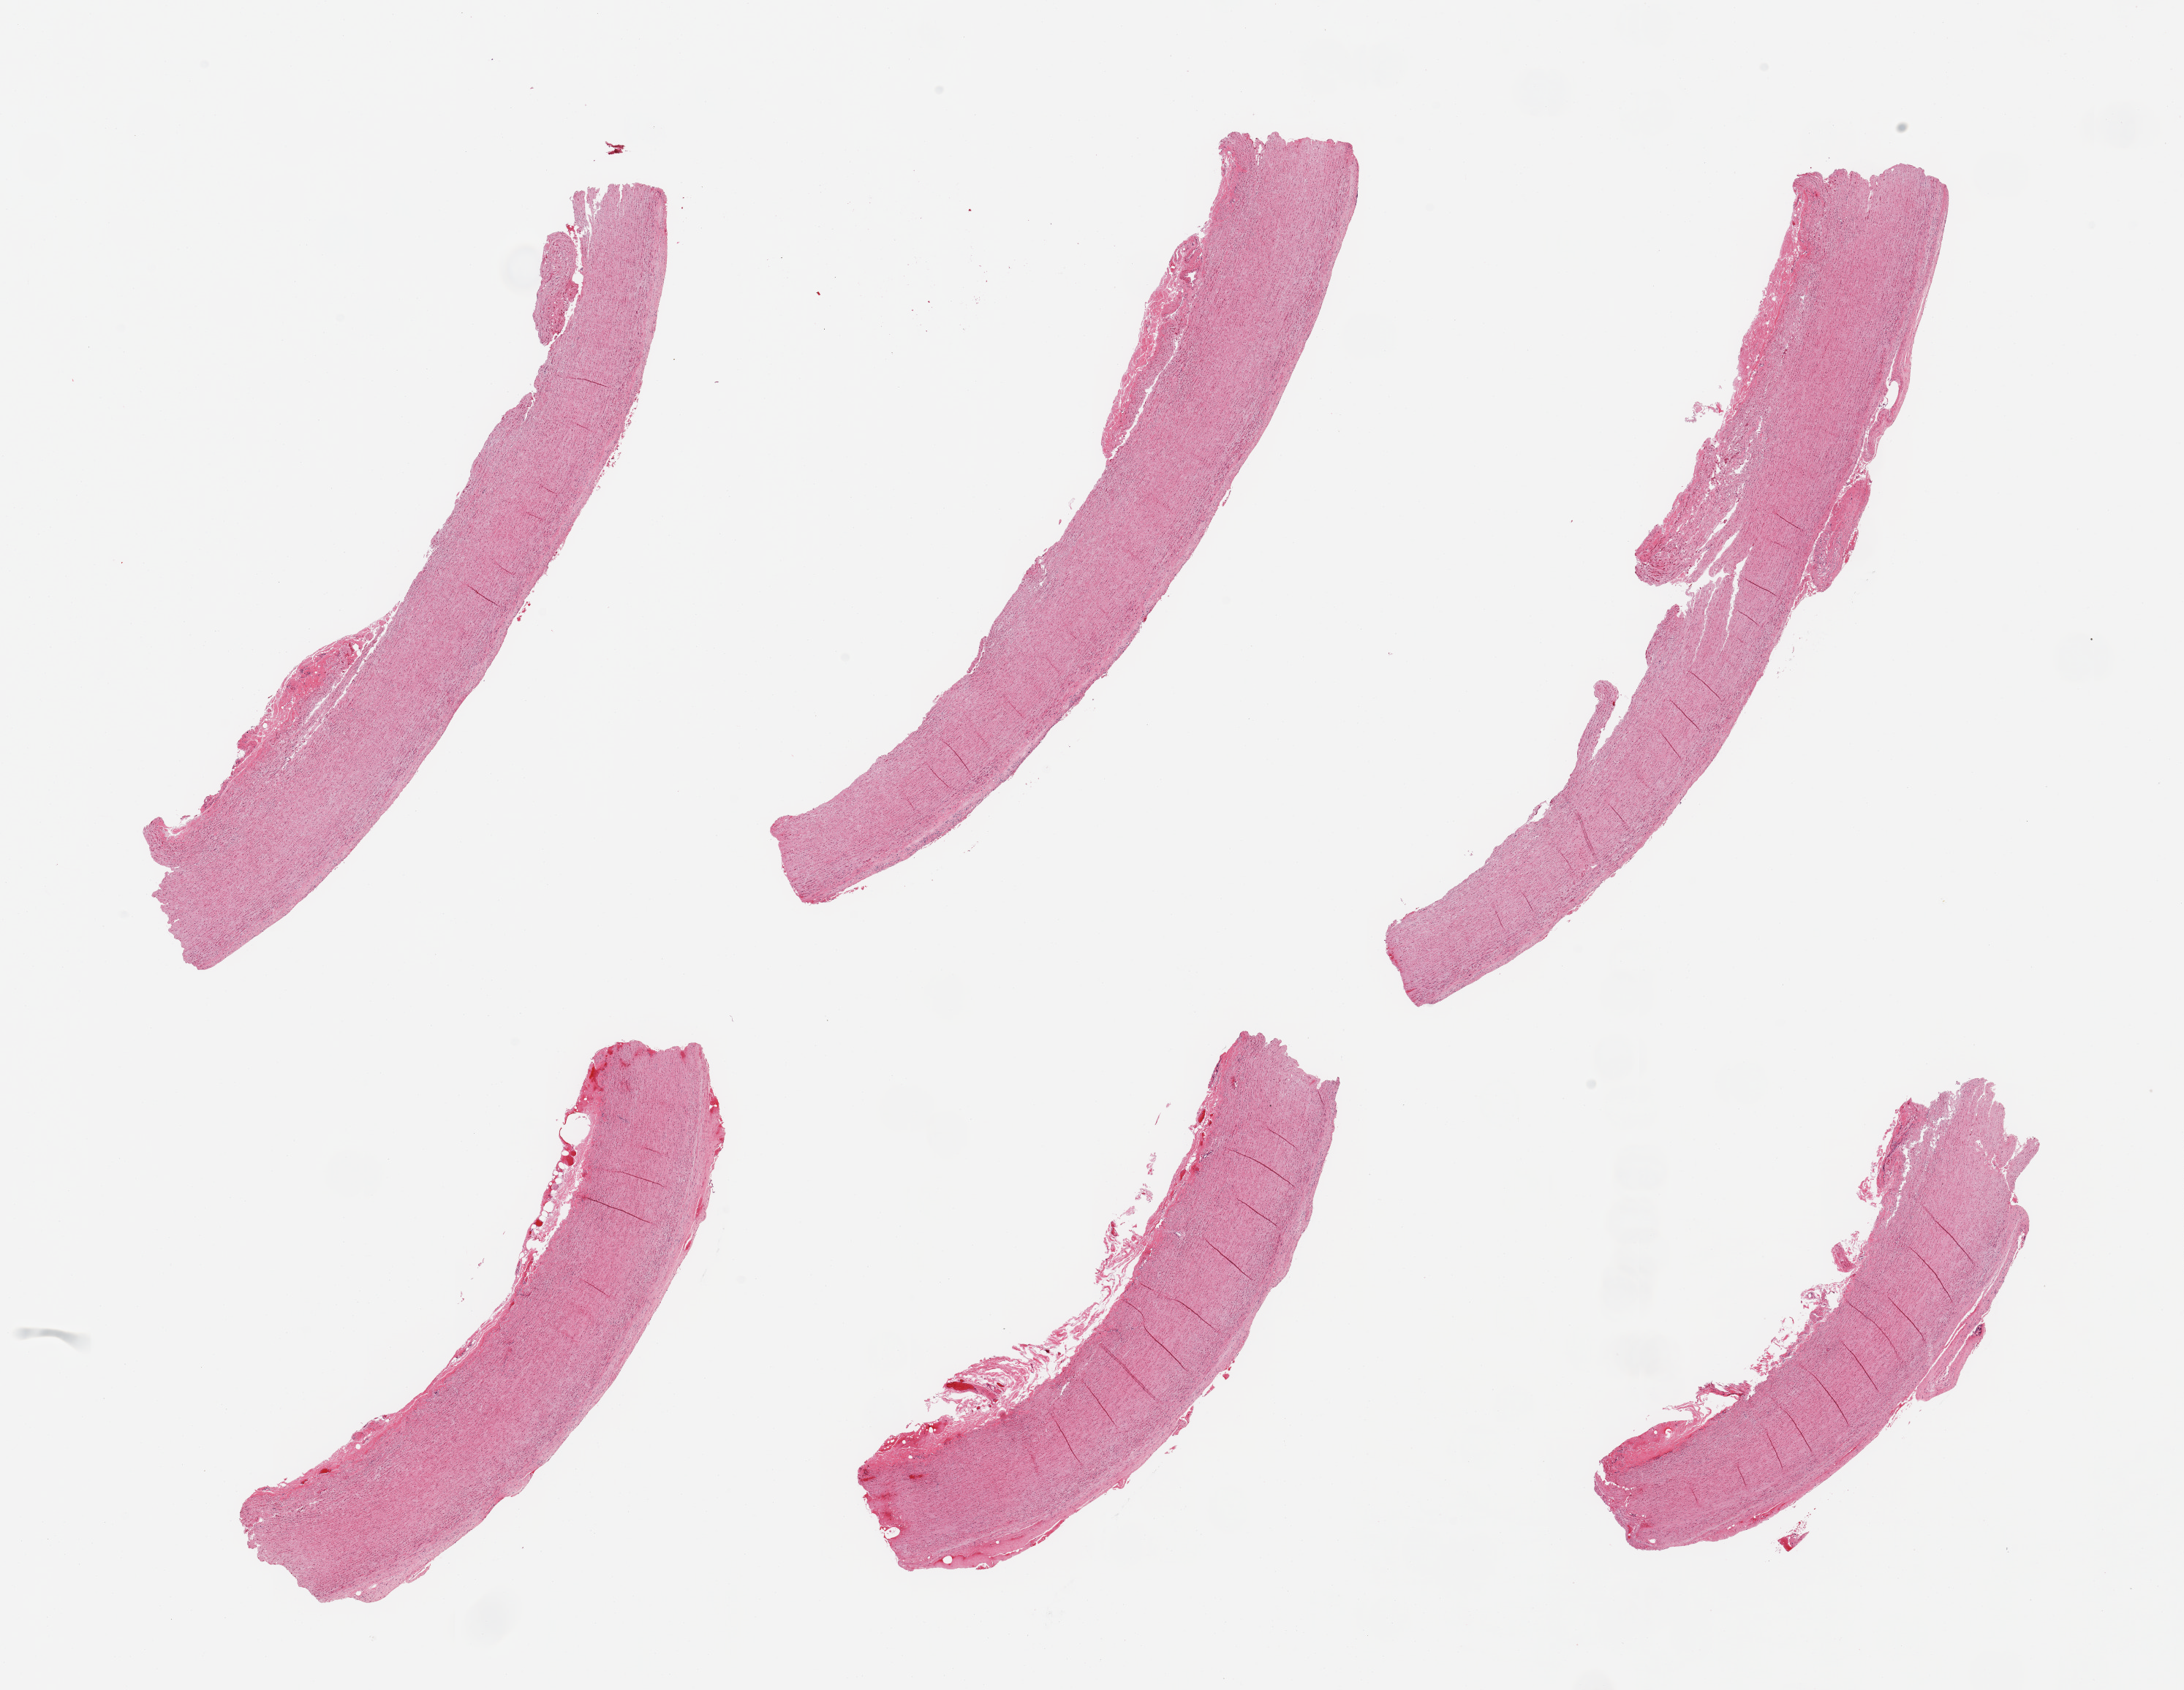
Digitized H&E-stained section, low-resolution overview of the scanned area, about 23.6 x 18.3 mm (slide scanned at 20x). PAXgene-fixed, paraffin-embedded tissue. Sampled site (target tissue): aorta. Donor tissue sample. Donor: male.
Reviewer comment on this tissue sample: 6 pieces; atherosclerosis.